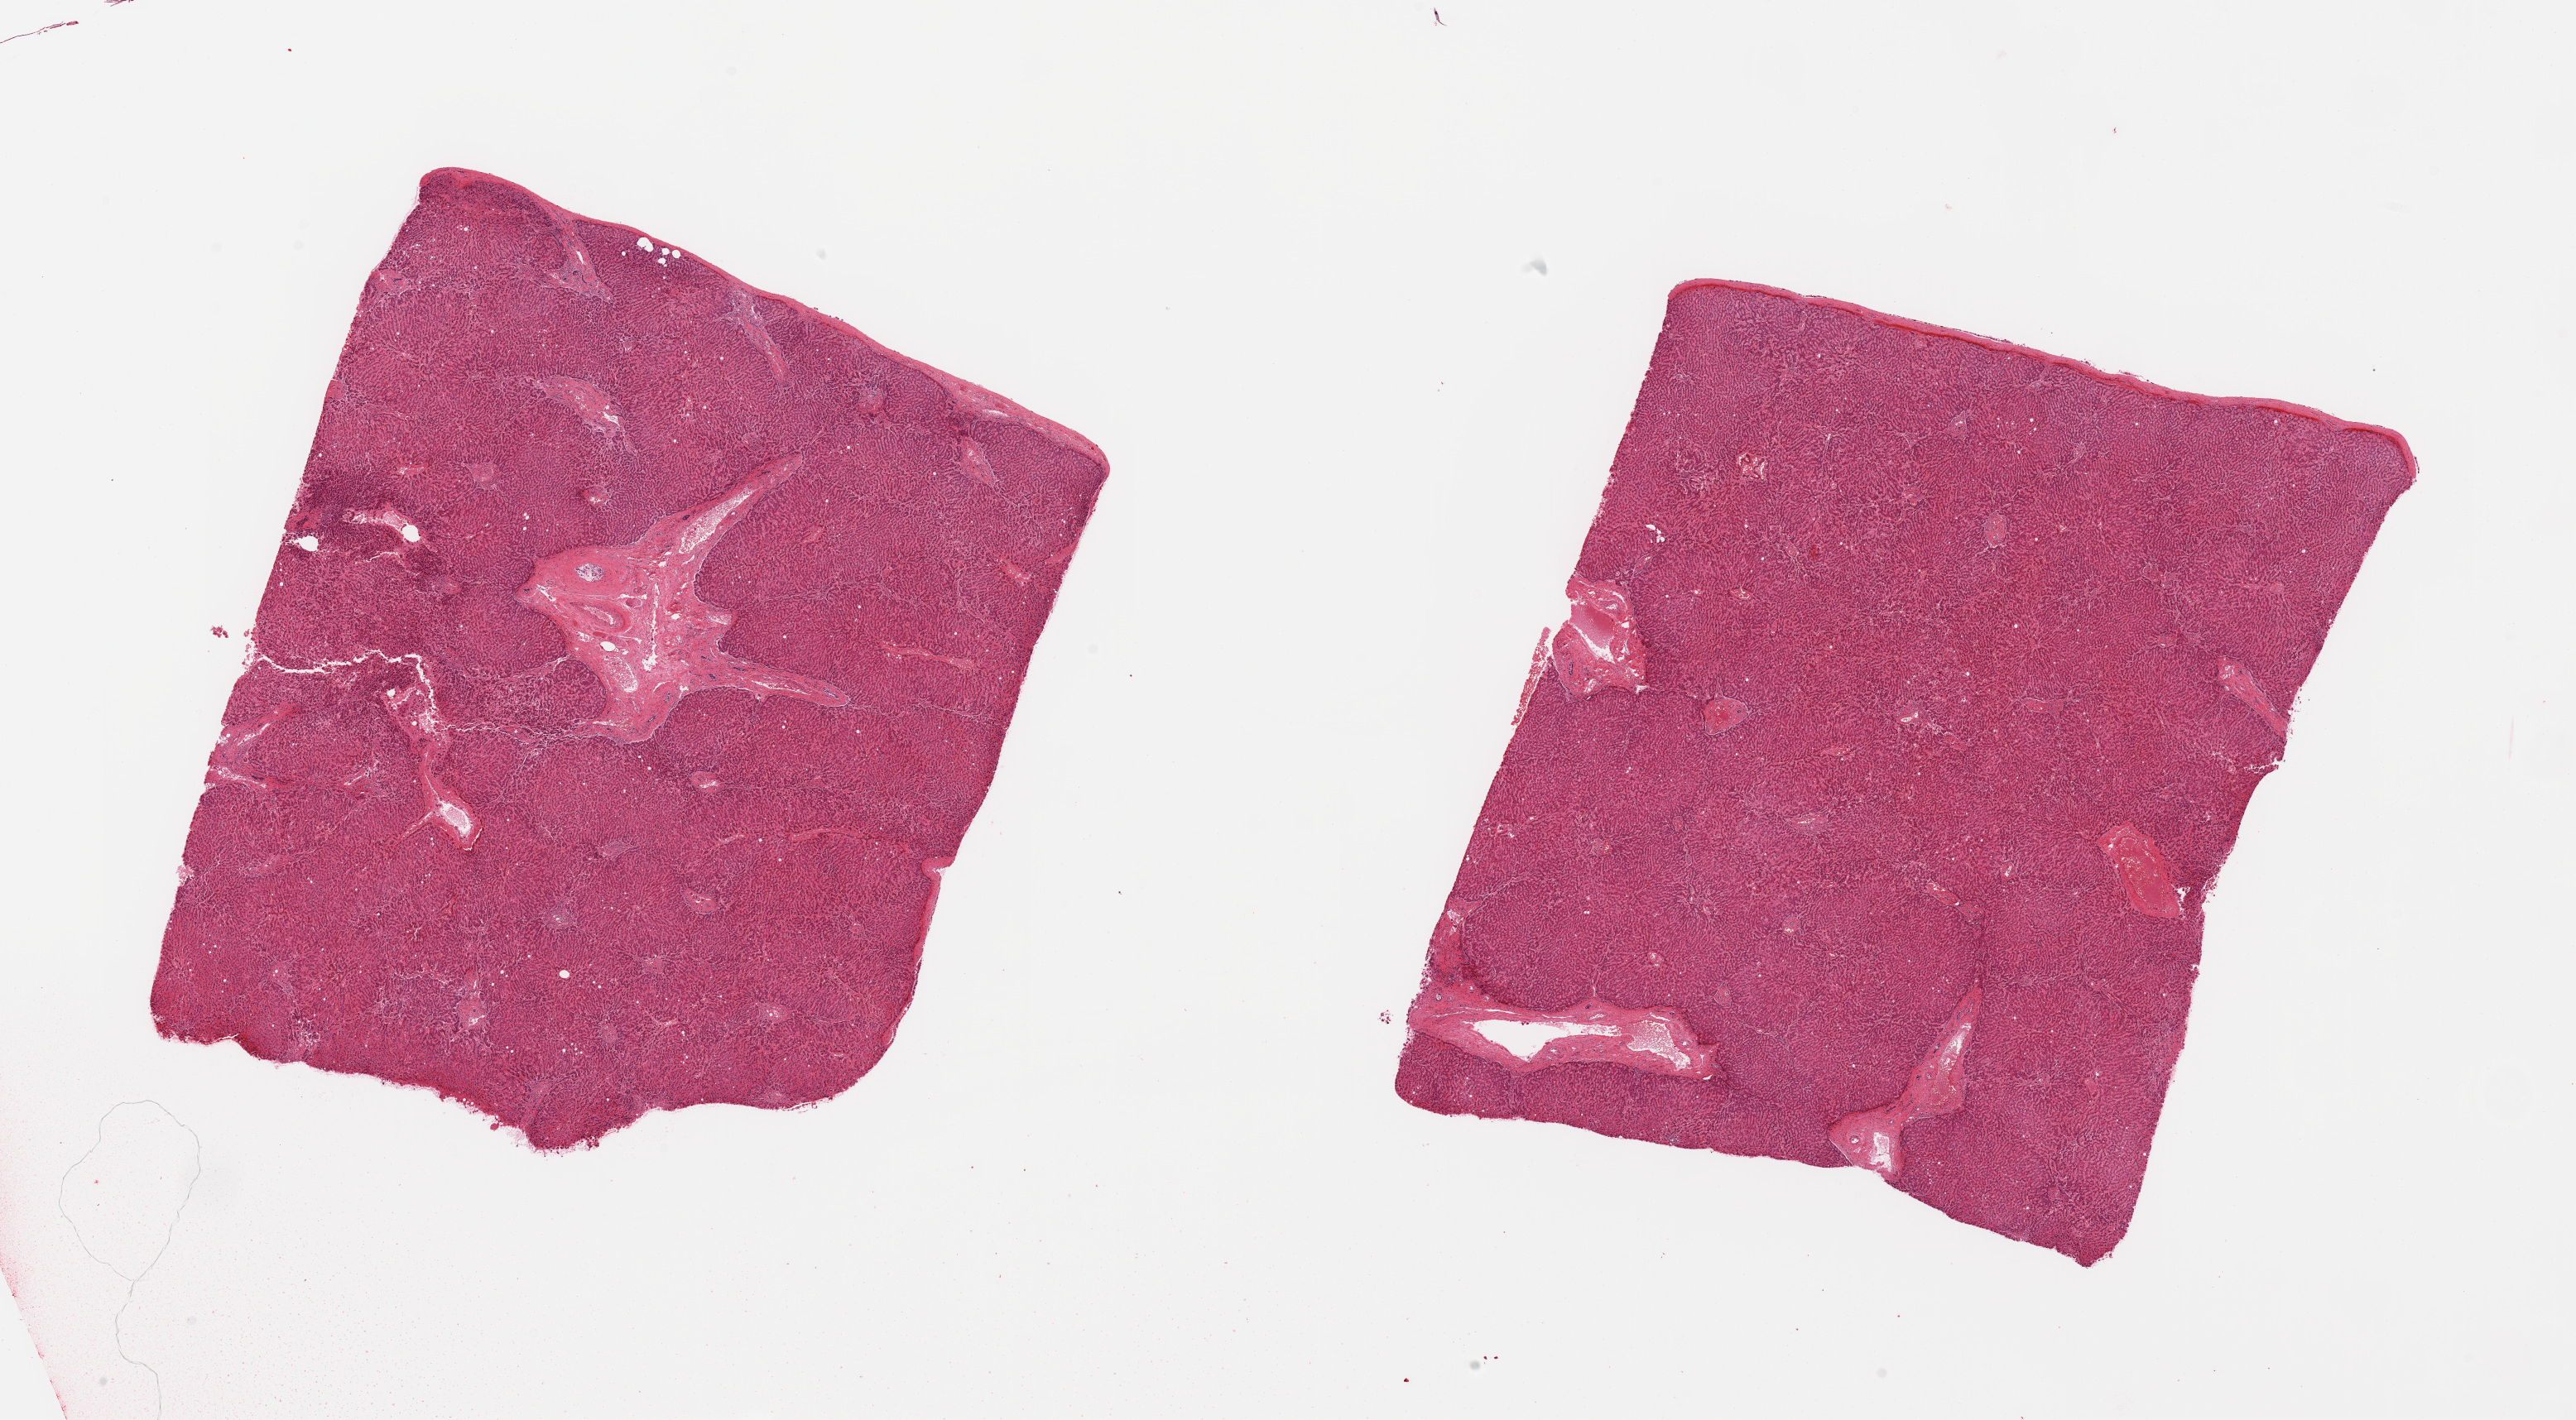
Whole-slide image, H&E stain, whole scanned area (about 24.6 x 13.6 mm) shown as a low-resolution overview; PAXgene-fixed paraffin-embedded (PFPE) section; target tissue: liver; tissue donor sample. Donor: male.
* reviewer comment on this tissue sample: 2 pieces; include capsule (target is 1cm below capsule), central congestion